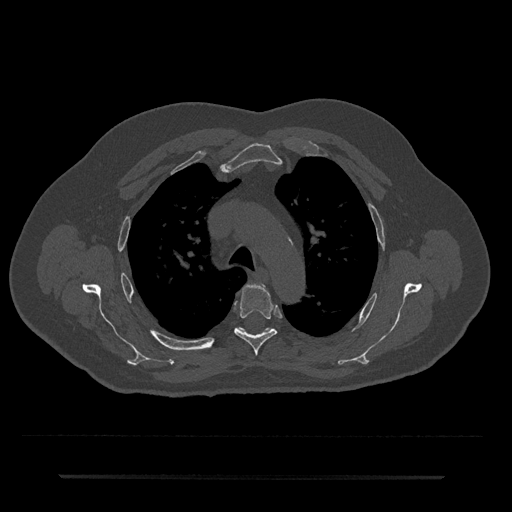
CT including the spine, one axial slice. Position 523 of 797 along the scan axis. Reconstruction kernel Br40s/3. 120 kVp. Bone window (W 1800 / L 400 HU). 0.5 mm slice thickness. 512 × 512 image matrix. Male patient, age 69 years. Case-level facts recorded for this patient, not image findings: primary cancer: prostate.
Structures marked on this image (semi-automatic segmentation, software-assisted and operator-edited):
- T4 vertebra: bounding box (x1, y1, x2, y2) in pixels: (234, 284, 277, 355)
- T5 vertebra: (237, 327, 272, 332)